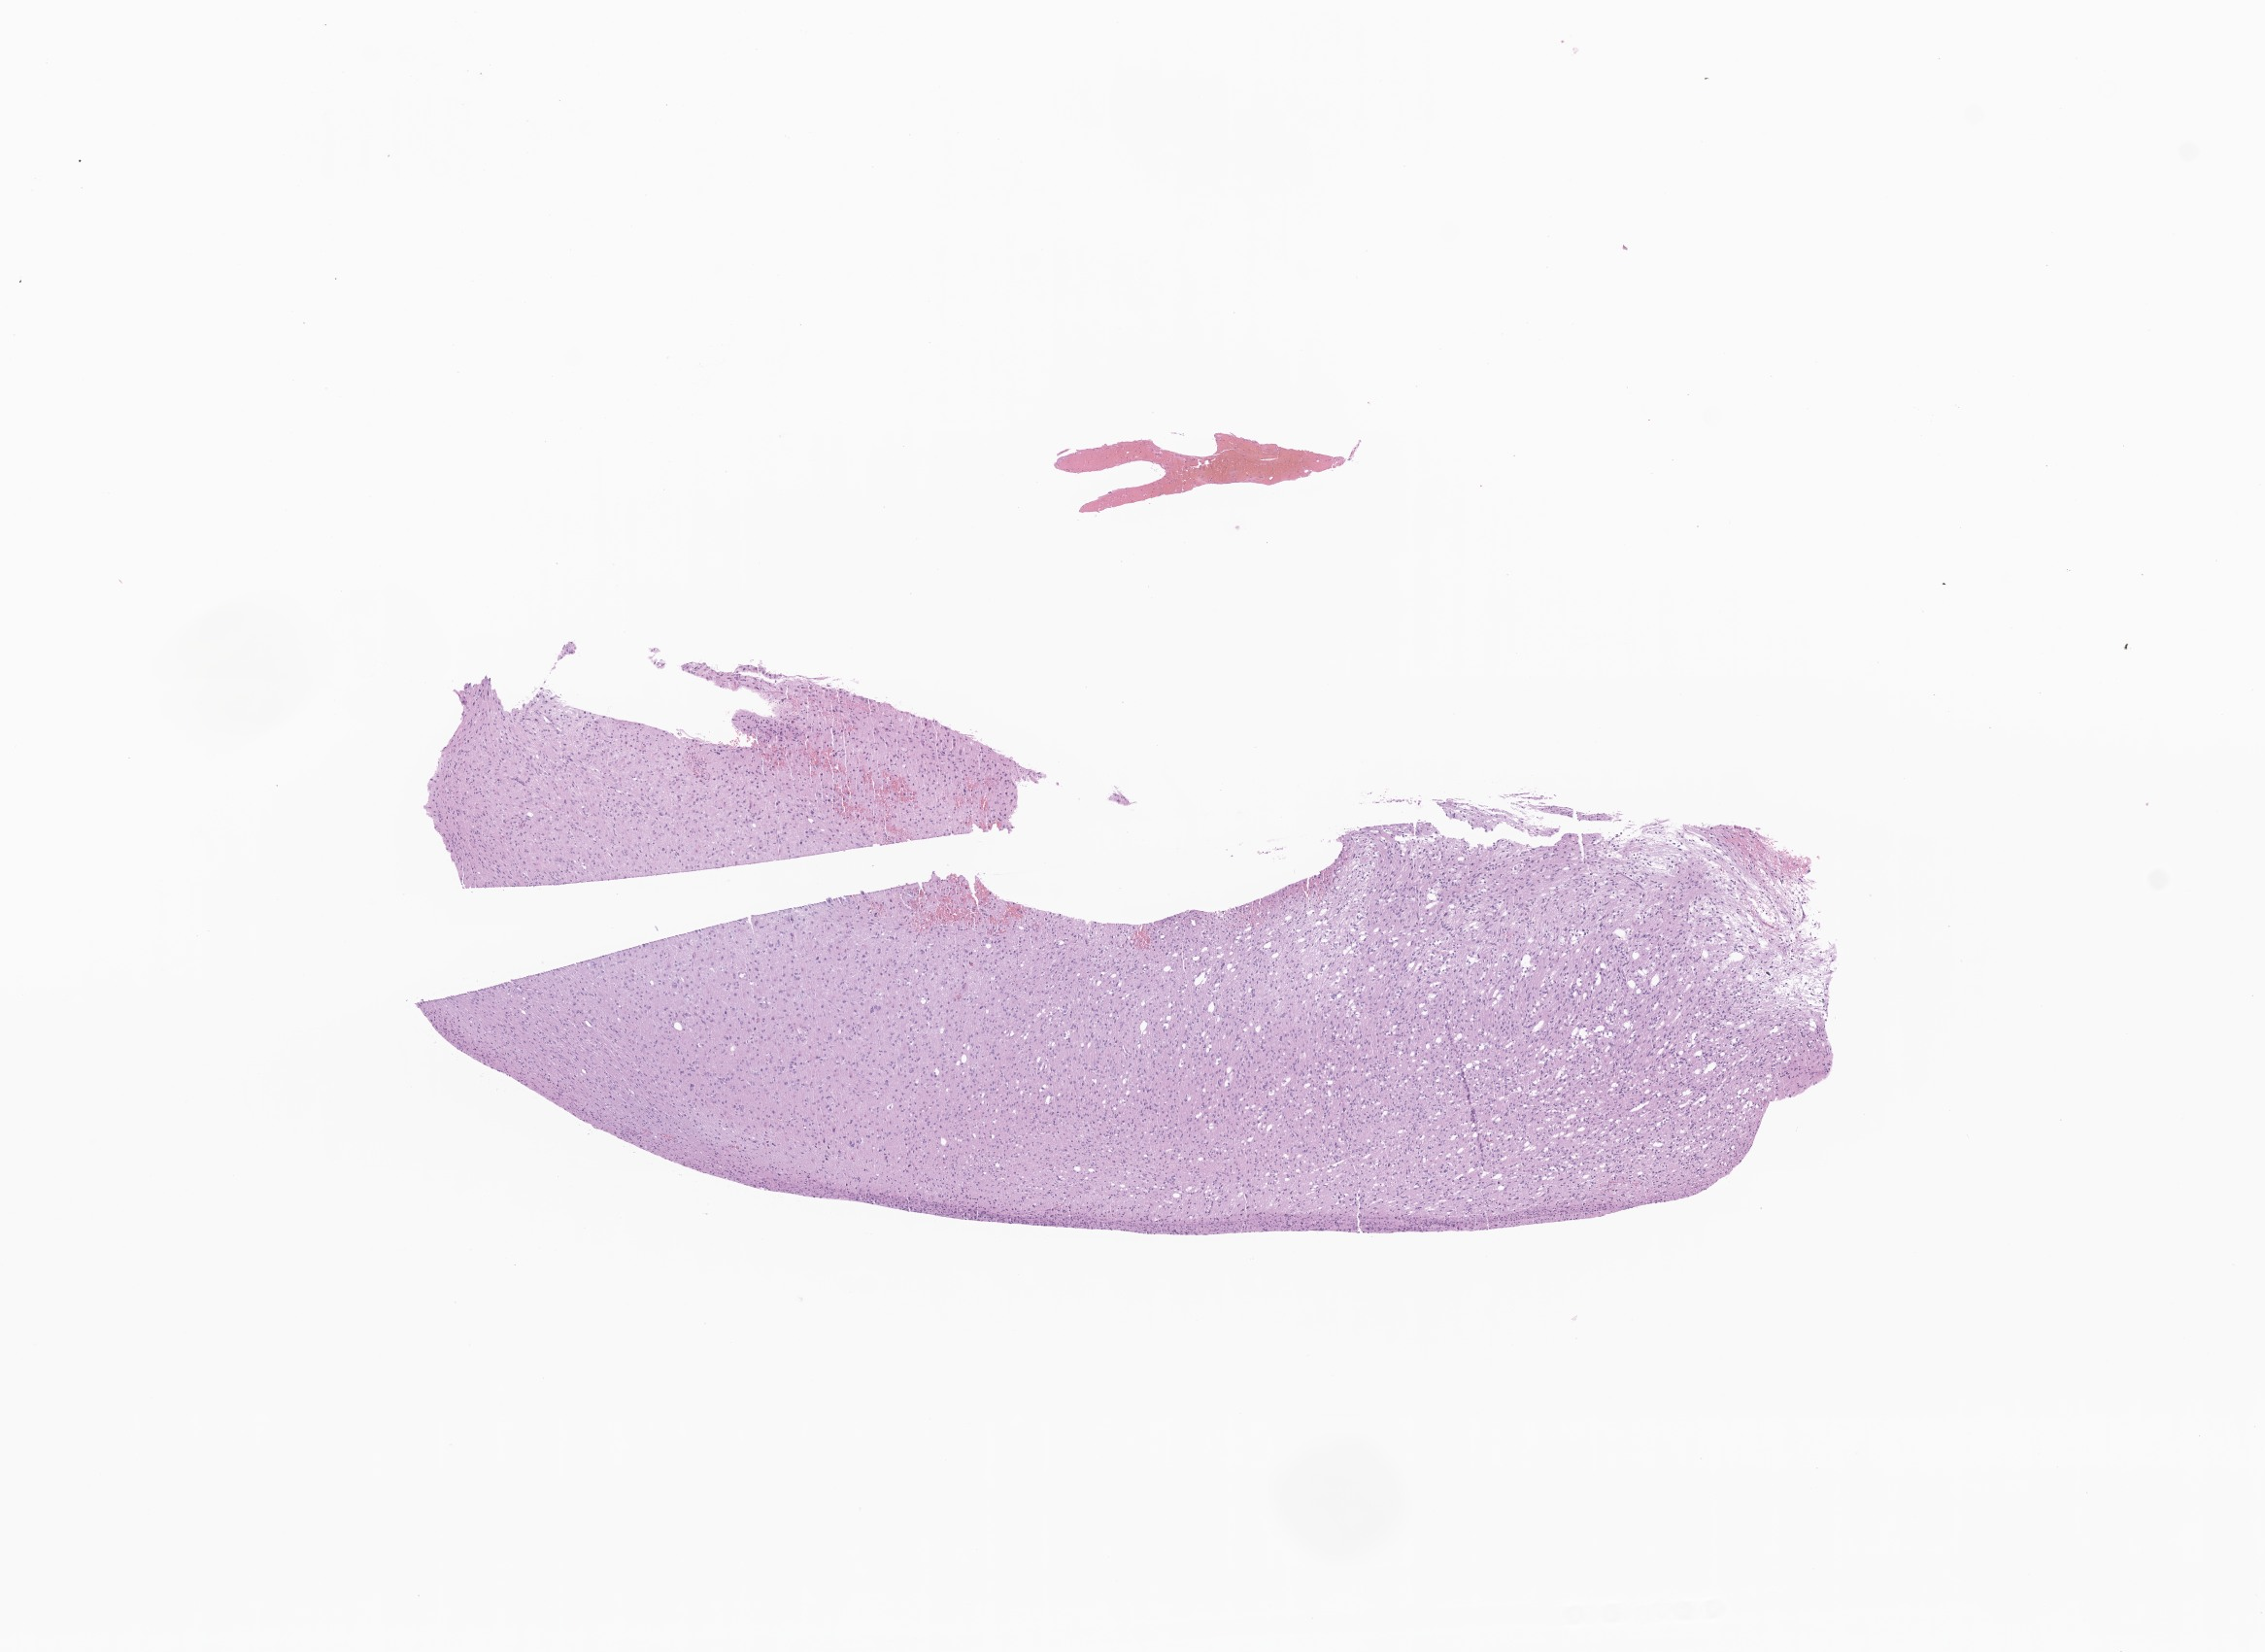
Whole-slide image, H&E stain of tumor tissue from the brain — a low-resolution overview of the entire scanned area, about 9.8 x 7.2 mm, formalin-fixed paraffin-embedded section. Patient: female, age 101 months (8 years 5 months).
* recorded diagnosis: Glioma, malignant